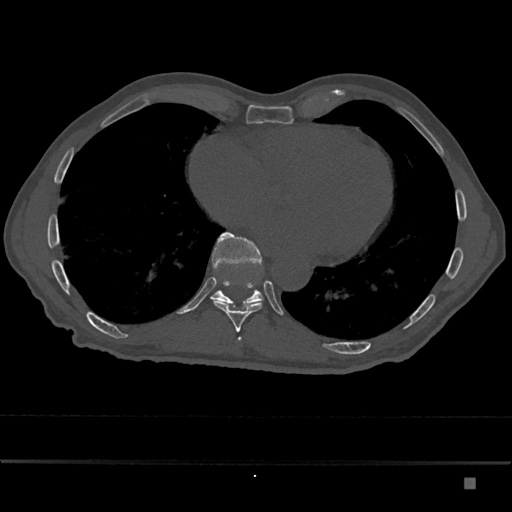
CT including the spine, one axial slice. 120 kVp. Bone window (W 1800 / L 400 HU). 0.5 mm slice thickness. 512 × 512 image matrix, field of view 390 × 390 mm. Male patient, age 72 years. From the clinical record (not read from this slice): primary cancer: prostate.
Structures marked on this image (semi-automatically segmented with operator editing):
- T10 vertebra: box from (x=210, y=232) to (x=264, y=307) px
- T9 vertebra: (x=213, y=300)–(x=263, y=333)